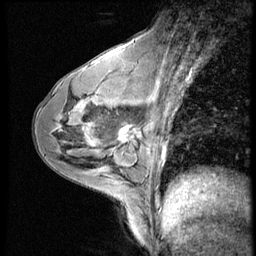
Breast MRI (dynamic contrast-enhanced), one sagittal slice. Position 34 of 56 along the scan axis. Dynamic contrast-enhanced series, image 2 of 4 at this slice position (ordered by acquisition). 1.5 T. TE 4.2 ms, TR 9 ms. 2.5 mm slice thickness. 256 × 256 image matrix. Female patient, age 43 years. Case-level facts recorded for this patient, not image findings: setting: breast cancer imaged before/during neoadjuvant chemotherapy; receptor status: HR-positive, HER2-negative.
Outlined on this slice (semi-automatically segmented with operator editing):
- analysis volume of interest (the breast-tissue region the enhancement analysis was run in; not a lesion): bounding box <104,104,152,159> (left, top, right, bottom; pixels)
- tumour enhancement mask (voxels above the 140 % enhancement threshold inside the analysis volume of interest): <120,126,134,143>